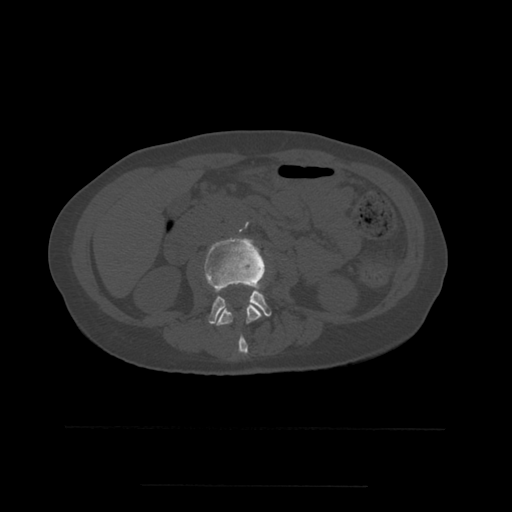
CT including the spine, one axial slice. Slice 198 of 544 in the series (ordered by position). Bone window (W 1800 / L 400 HU). 512 × 512 image matrix. Patient age 58 years. Case-level facts recorded for this patient, not image findings: primary cancer: lung.
Structures marked on this image (semi-automatic segmentation, software-assisted and operator-edited):
- L2 vertebra: bounding box (x1, y1, x2, y2) in pixels: (217, 238, 262, 355)
- L3 vertebra: (205, 237, 272, 325)